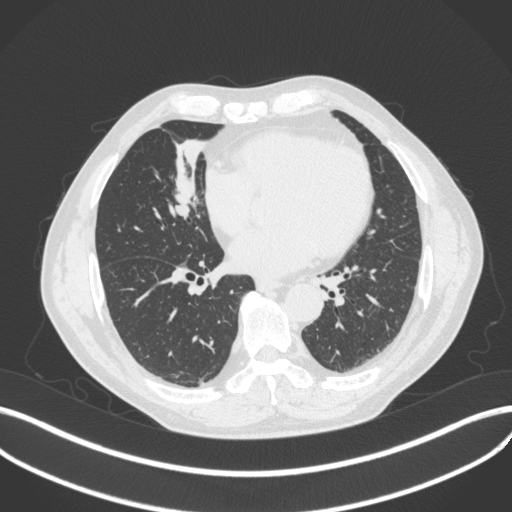
Chest CT, one axial slice. Position 163 of 429 along the scan axis. Reconstruction kernel B31f. 120 kVp. Lung window (W 1500 / L -600 HU). 1 mm slice thickness. 512 × 512 image matrix, field of view 400 × 400 mm. Patient: male, 61 years. Case-level facts recorded for this patient, not image findings: clinical TNM (as recorded): T2b N1 M0.
Annotated regions visible in this slice (rectangle marked by the reading radiologist):
- lung tumour (recorded histology: squamous cell carcinoma): bounding box <164,164,208,226> (left, top, right, bottom; pixels)